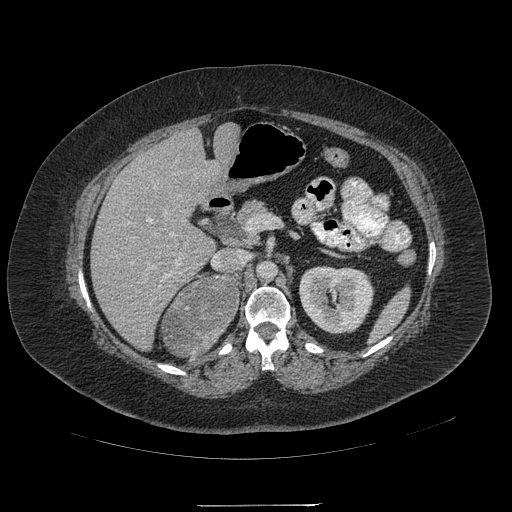
Contrast-enhanced abdominal CT, one axial slice; position 120 of 217 along the scan axis; reconstruction kernel STANDARD; 120 kVp; intravenous contrast given; soft-tissue window (W 400 / L 40 HU); 1.25 mm slice thickness; 512 × 512 image matrix, field of view 453 × 453 mm. Female patient, age 55 years. Case-level facts recorded for this patient, not image findings: diagnosis: adrenocortical carcinoma; tumour side: right adrenal.
Structures marked on this image (semi-automatically segmented with operator editing):
- mass: bounding box (x1, y1, x2, y2) in pixels: (162, 277, 239, 357)